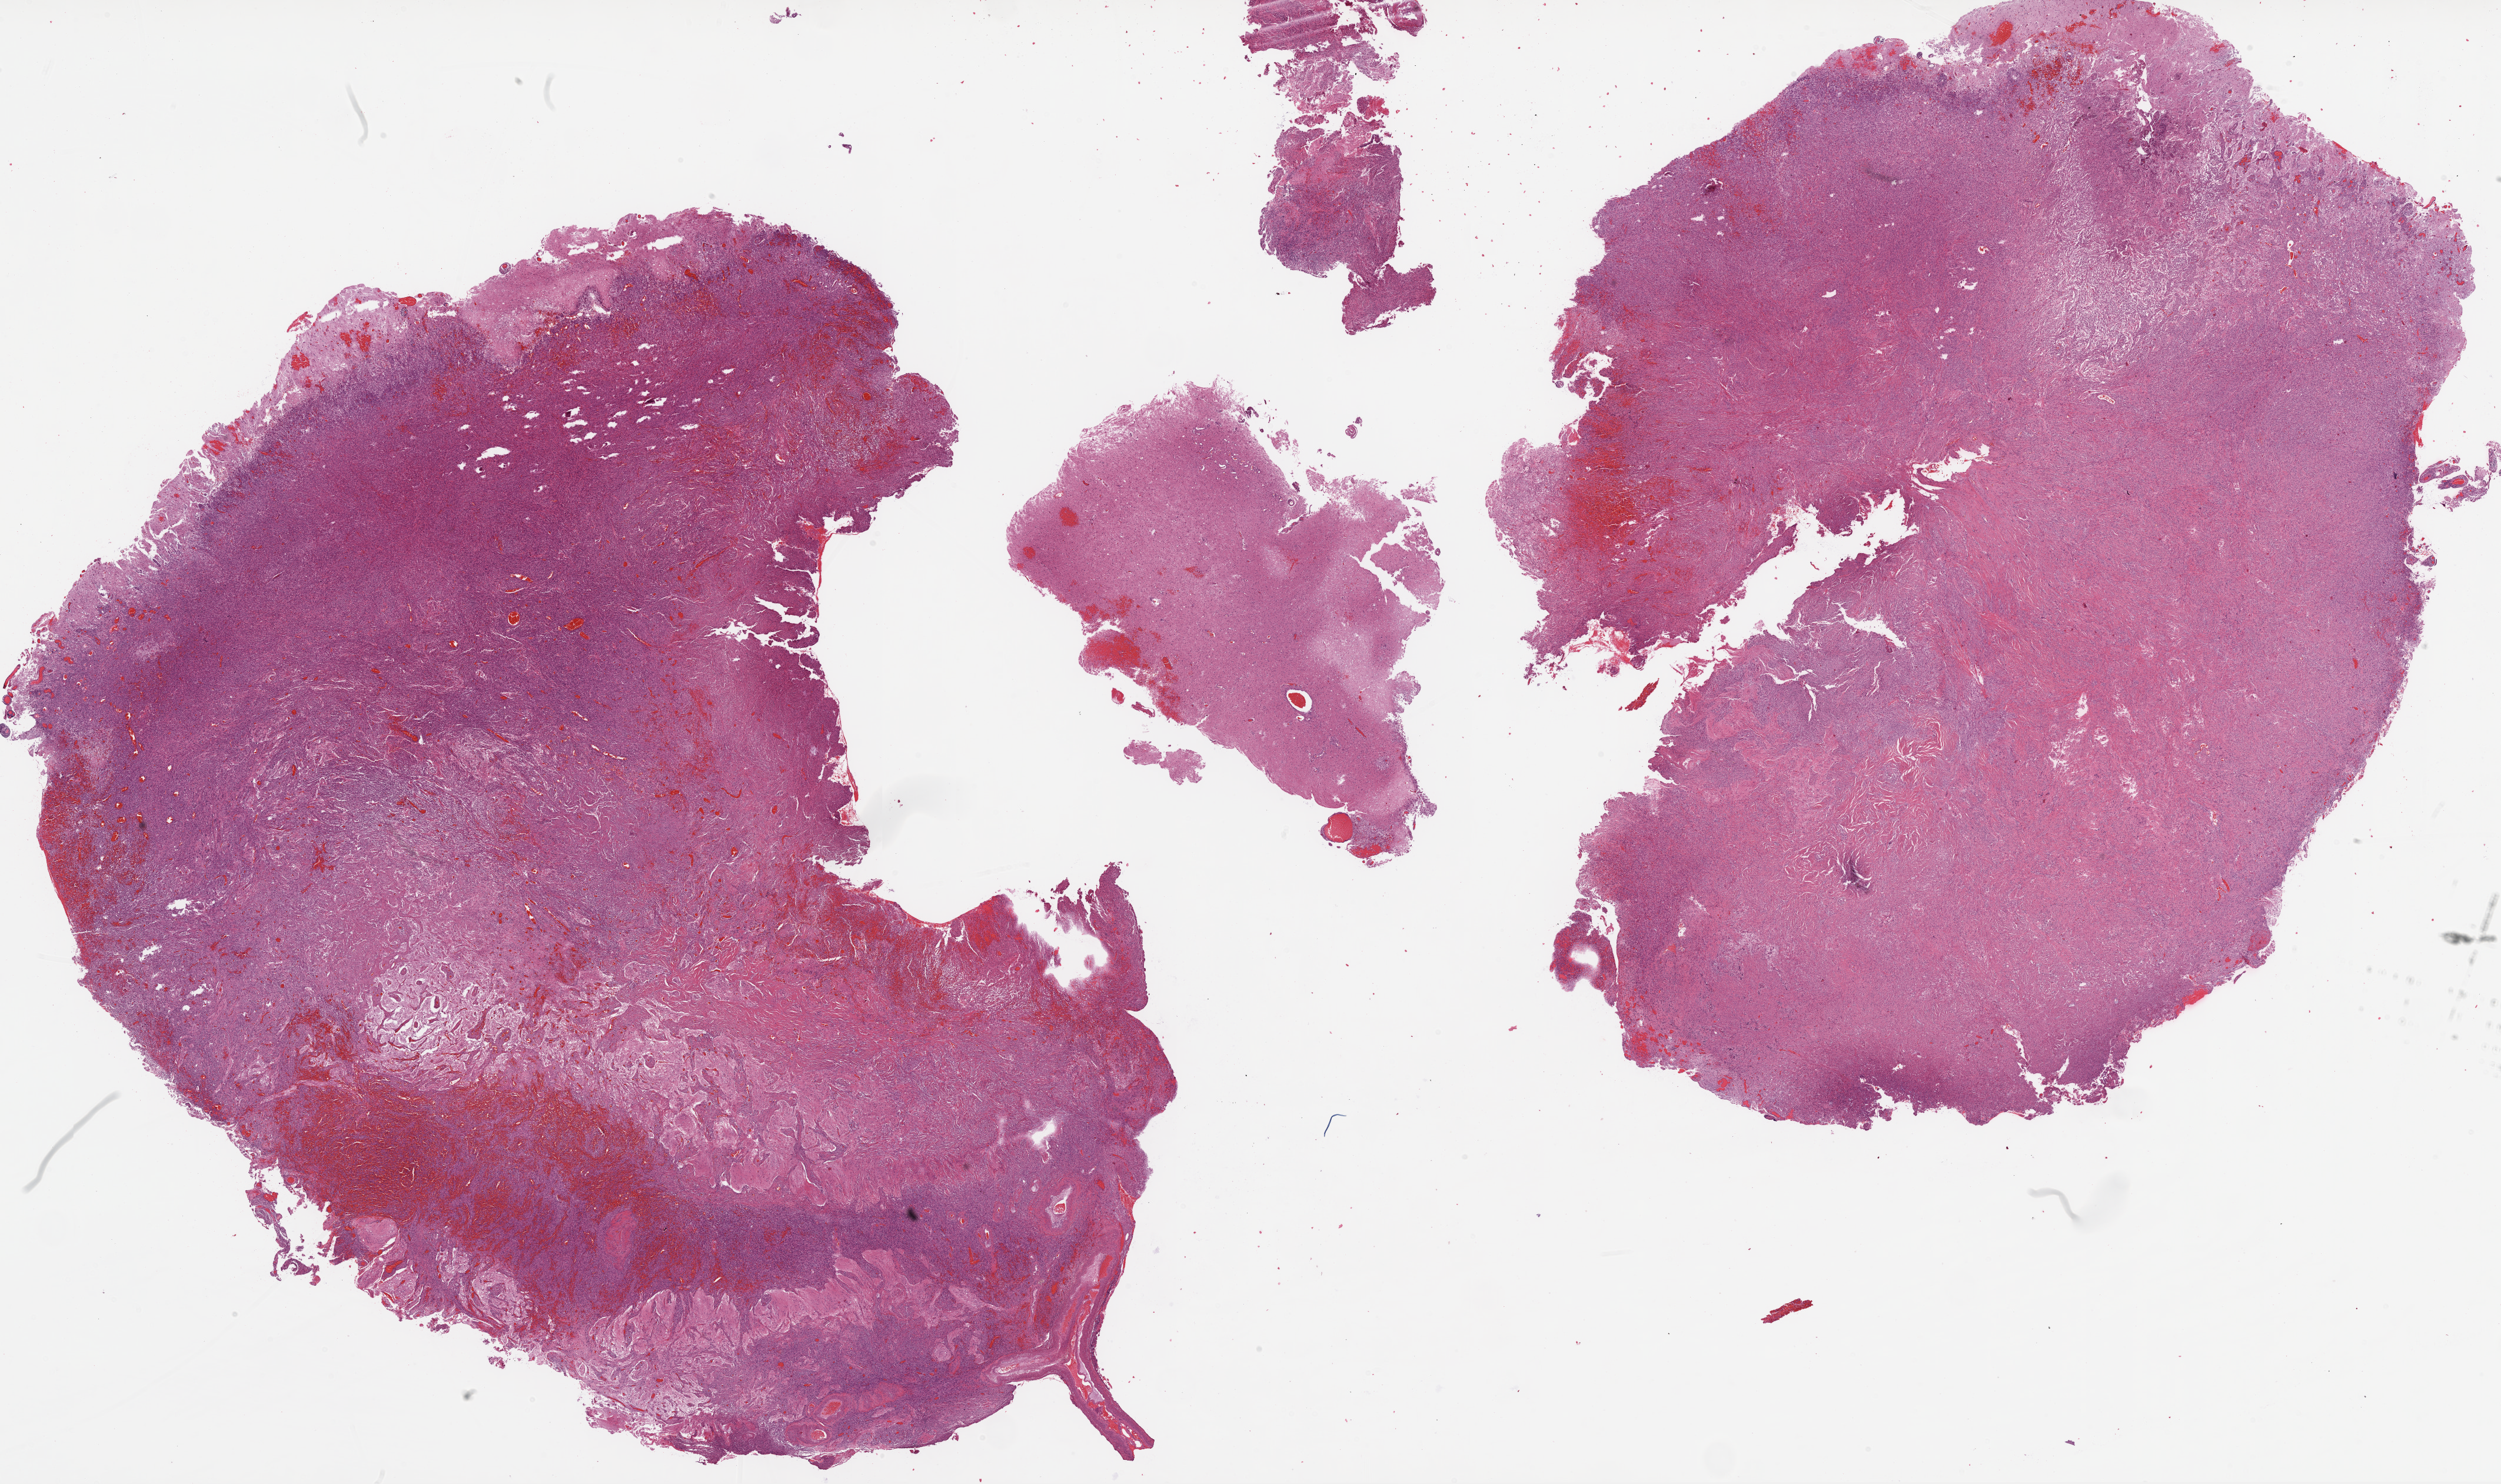
Digitized H&E tissue section (whole slide) — whole scanned area (about 34.1 x 20.2 mm, acquisition: 20x scan) shown as a low-resolution overview. FFPE section. Sample: primary tumour, brain. Patient: male, age at initial diagnosis 47 years.
Histologic diagnosis: Glioblastoma.